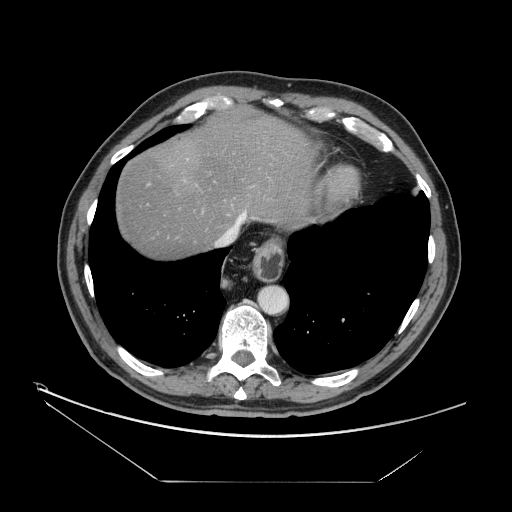
Contrast-enhanced abdominal CT, one axial slice. Position 139 of 161 along the scan axis. Reconstruction kernel STANDARD. Intravenous contrast given. Soft-tissue window (W 400 / L 40 HU). 2.5 mm slice thickness. 512 × 512 image matrix, field of view 440 × 440 mm. Male patient, age 65 years. Case-level facts recorded for this patient, not image findings: diagnosis: colorectal cancer liver metastases, imaged before liver resection; multiple liver metastases: yes; largest metastasis: 4.2 cm; disease in both lobes: yes.
Outlined on this slice (manually delineated by an expert):
- hepatic veins: bounding box (x1, y1, x2, y2) in pixels: (220, 211, 248, 244)
- liver: (115, 109, 315, 257)
- planned liver remnant (the part of the liver to remain after resection): (115, 109, 315, 257)
- portal vein (with intrahepatic branches): (187, 159, 218, 243)